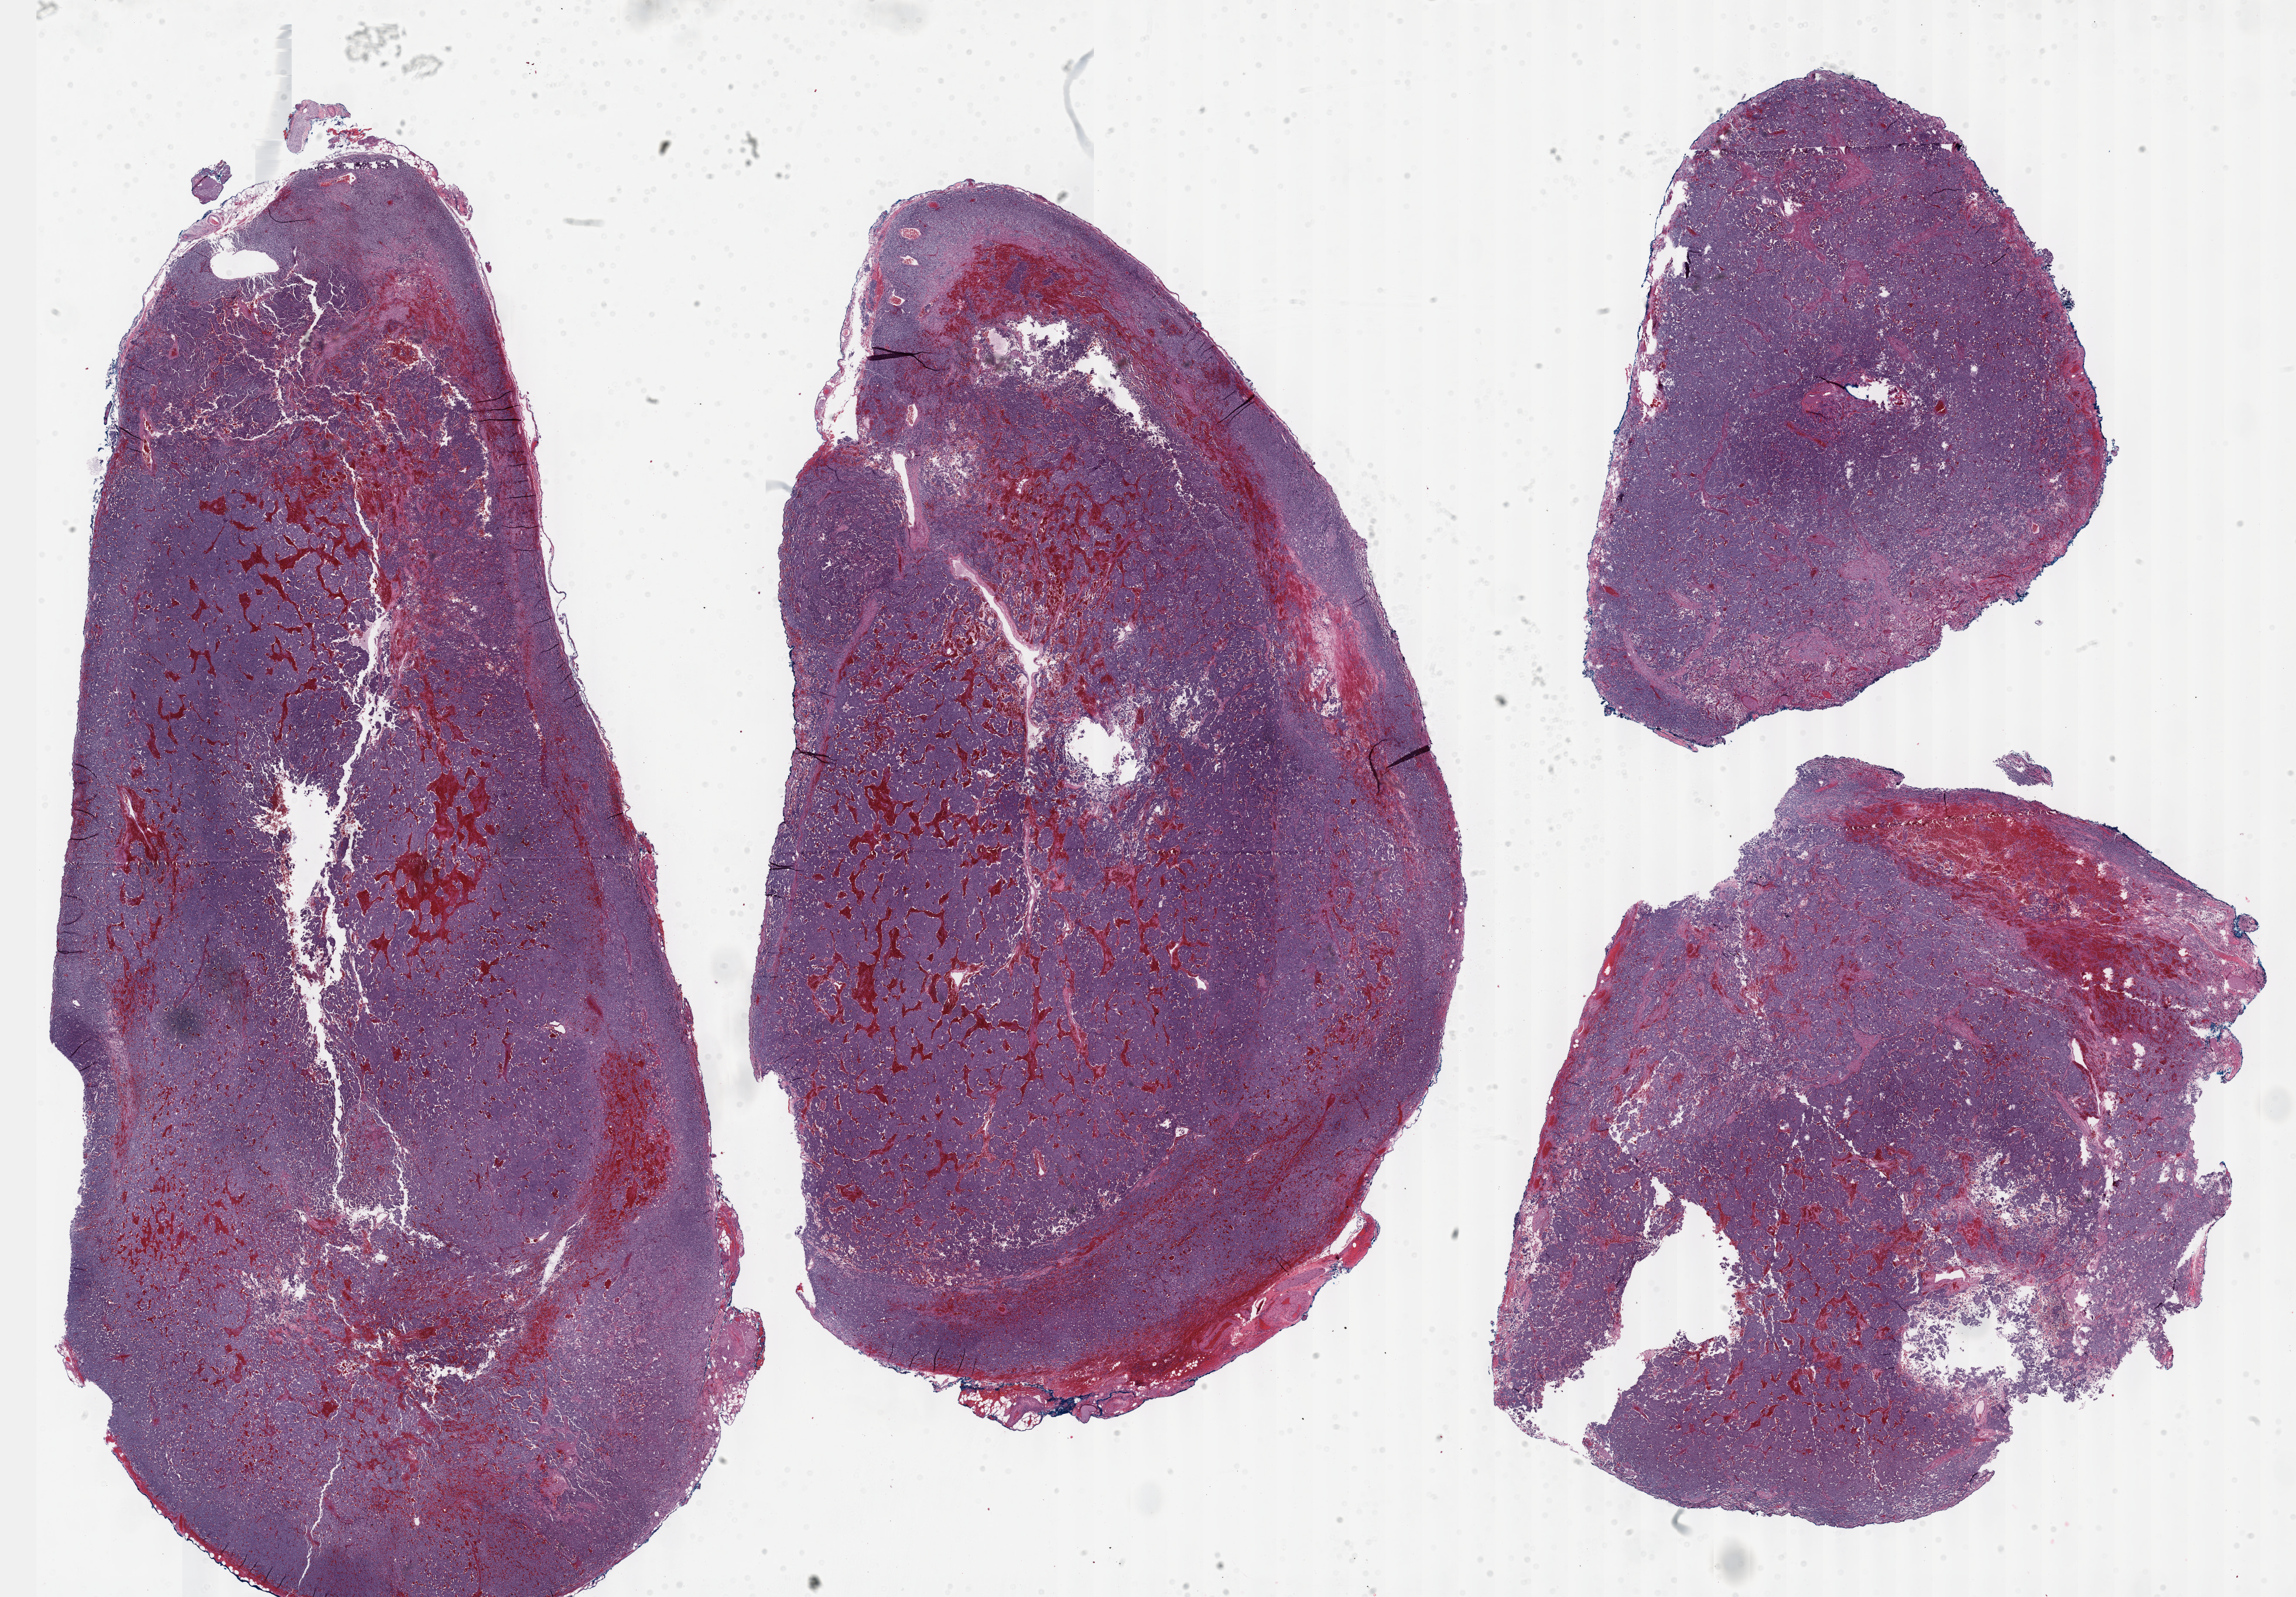
H&E-stained whole-slide image — whole scanned area (about 31.7 x 22.0 mm) shown as a low-resolution overview; formalin-fixed paraffin-embedded (FFPE) diagnostic section; primary tumour sample from the other endocrine glands and related structures. Female patient; age at initial diagnosis 61 years.
Pathologic diagnosis: Pheochromocytoma, malignant (aortic body and other paraganglia).